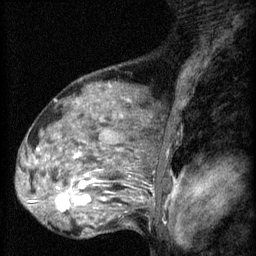
Breast MRI (dynamic contrast-enhanced), one sagittal slice; position 41 of 60 along the scan axis; 3 images stored at this slice position (order not interpretable as contrast timing); 1.5 T; TE 4.2 ms, TR 8.2 ms; 2 mm slice thickness; 256 × 256 image matrix, field of view 180 × 180 mm. Female patient, age 48 years.
Structures marked on this image (semi-automatically segmented with operator editing):
- analysis volume of interest (the breast-tissue region the enhancement analysis was run in; not a lesion): bounding box <48,160,125,217> (left, top, right, bottom; pixels)
- tumour enhancement mask (voxels above the 70 % enhancement threshold inside the analysis volume of interest): <56,182,86,211>